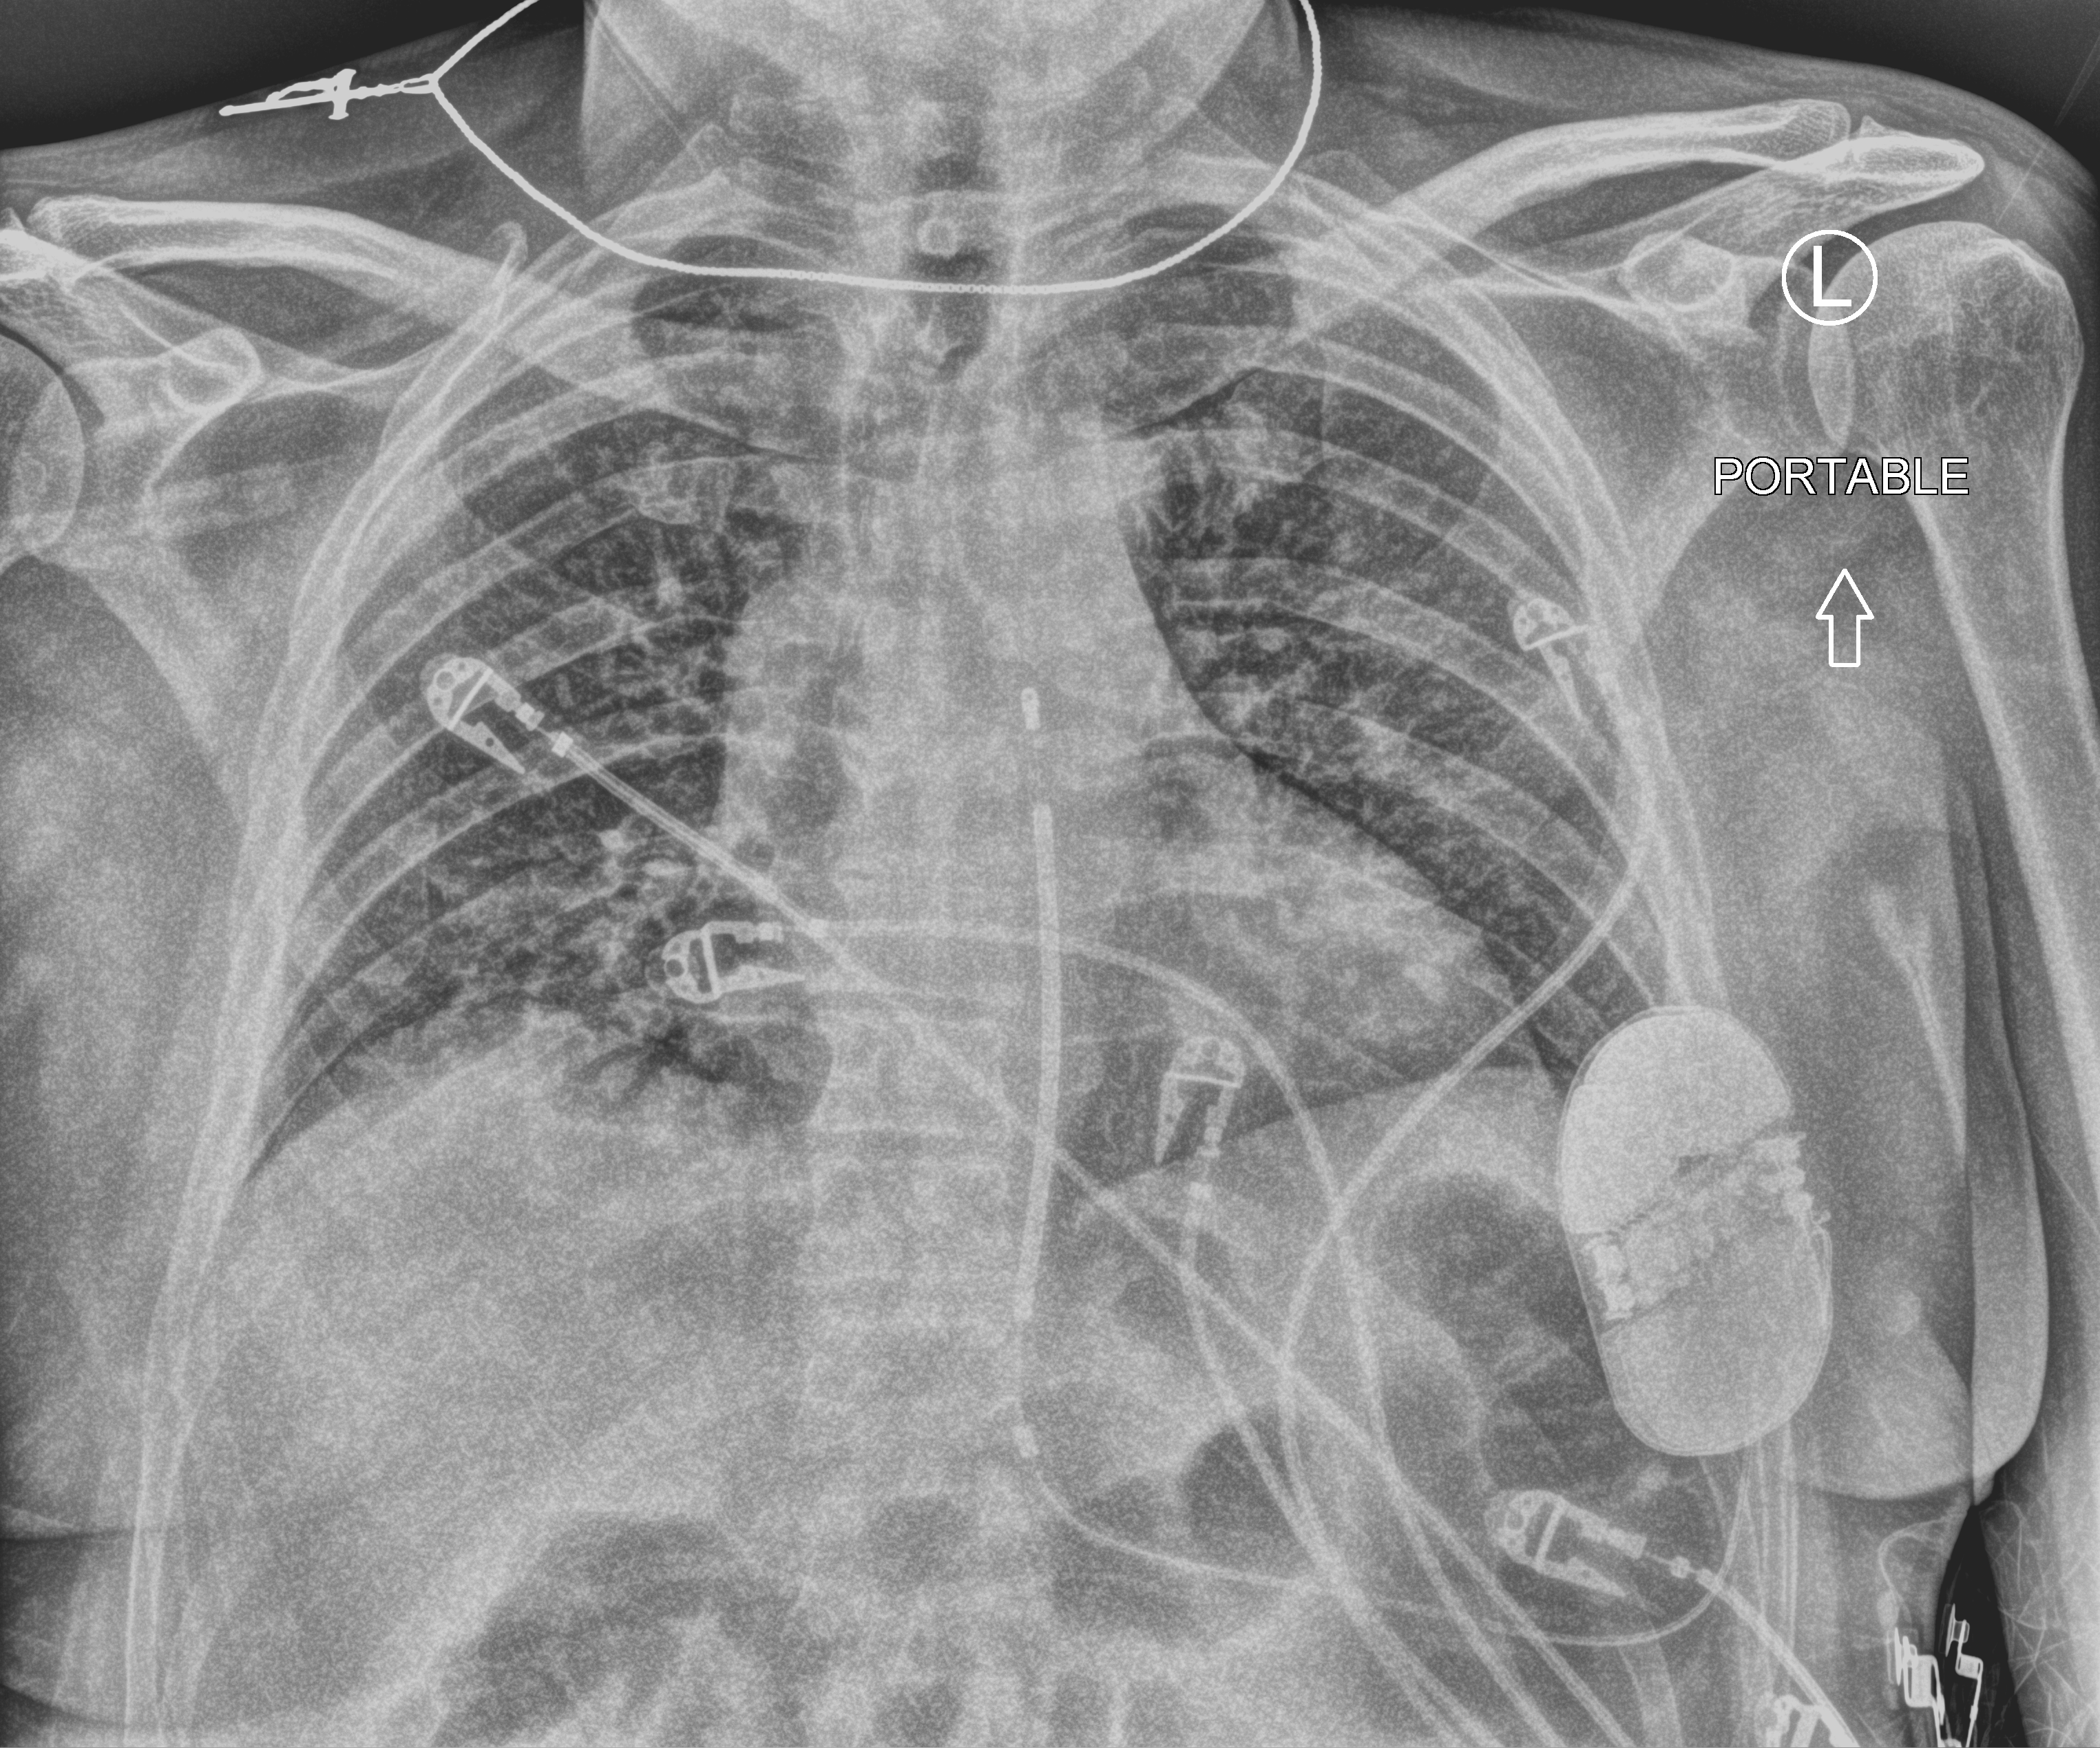
Portable chest radiograph. Patient hospitalised with COVID-19; male, aged 18–59 years.
From the hospital-stay record, not from the radiograph (when in the stay this image was taken is not recorded): length of hospital stay: 19 days; chronic kidney disease (admission record): no; admitted to intensive care during this hospital stay: no.